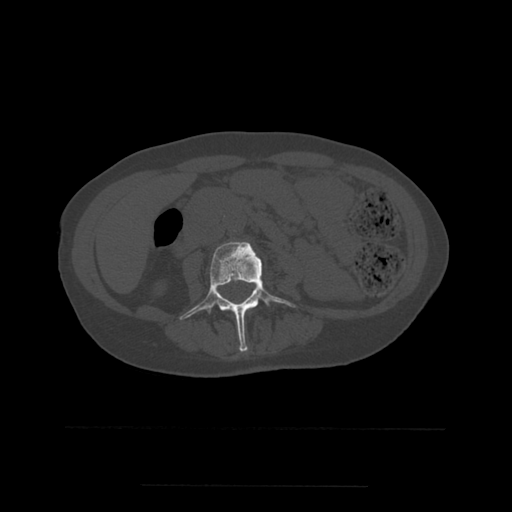
CT including the spine, one axial slice. Position 189 of 544 along the scan axis. Bone window (W 1800 / L 400 HU). 512 × 512 image matrix, field of view 350 × 350 mm. Patient age 58 years. From the clinical record (not read from this slice): primary cancer: lung.
Annotated regions visible in this slice (semi-automatically segmented with operator editing):
- L3 vertebra: bounding box [x1, y1, x2, y2] px = [180, 242, 296, 352]